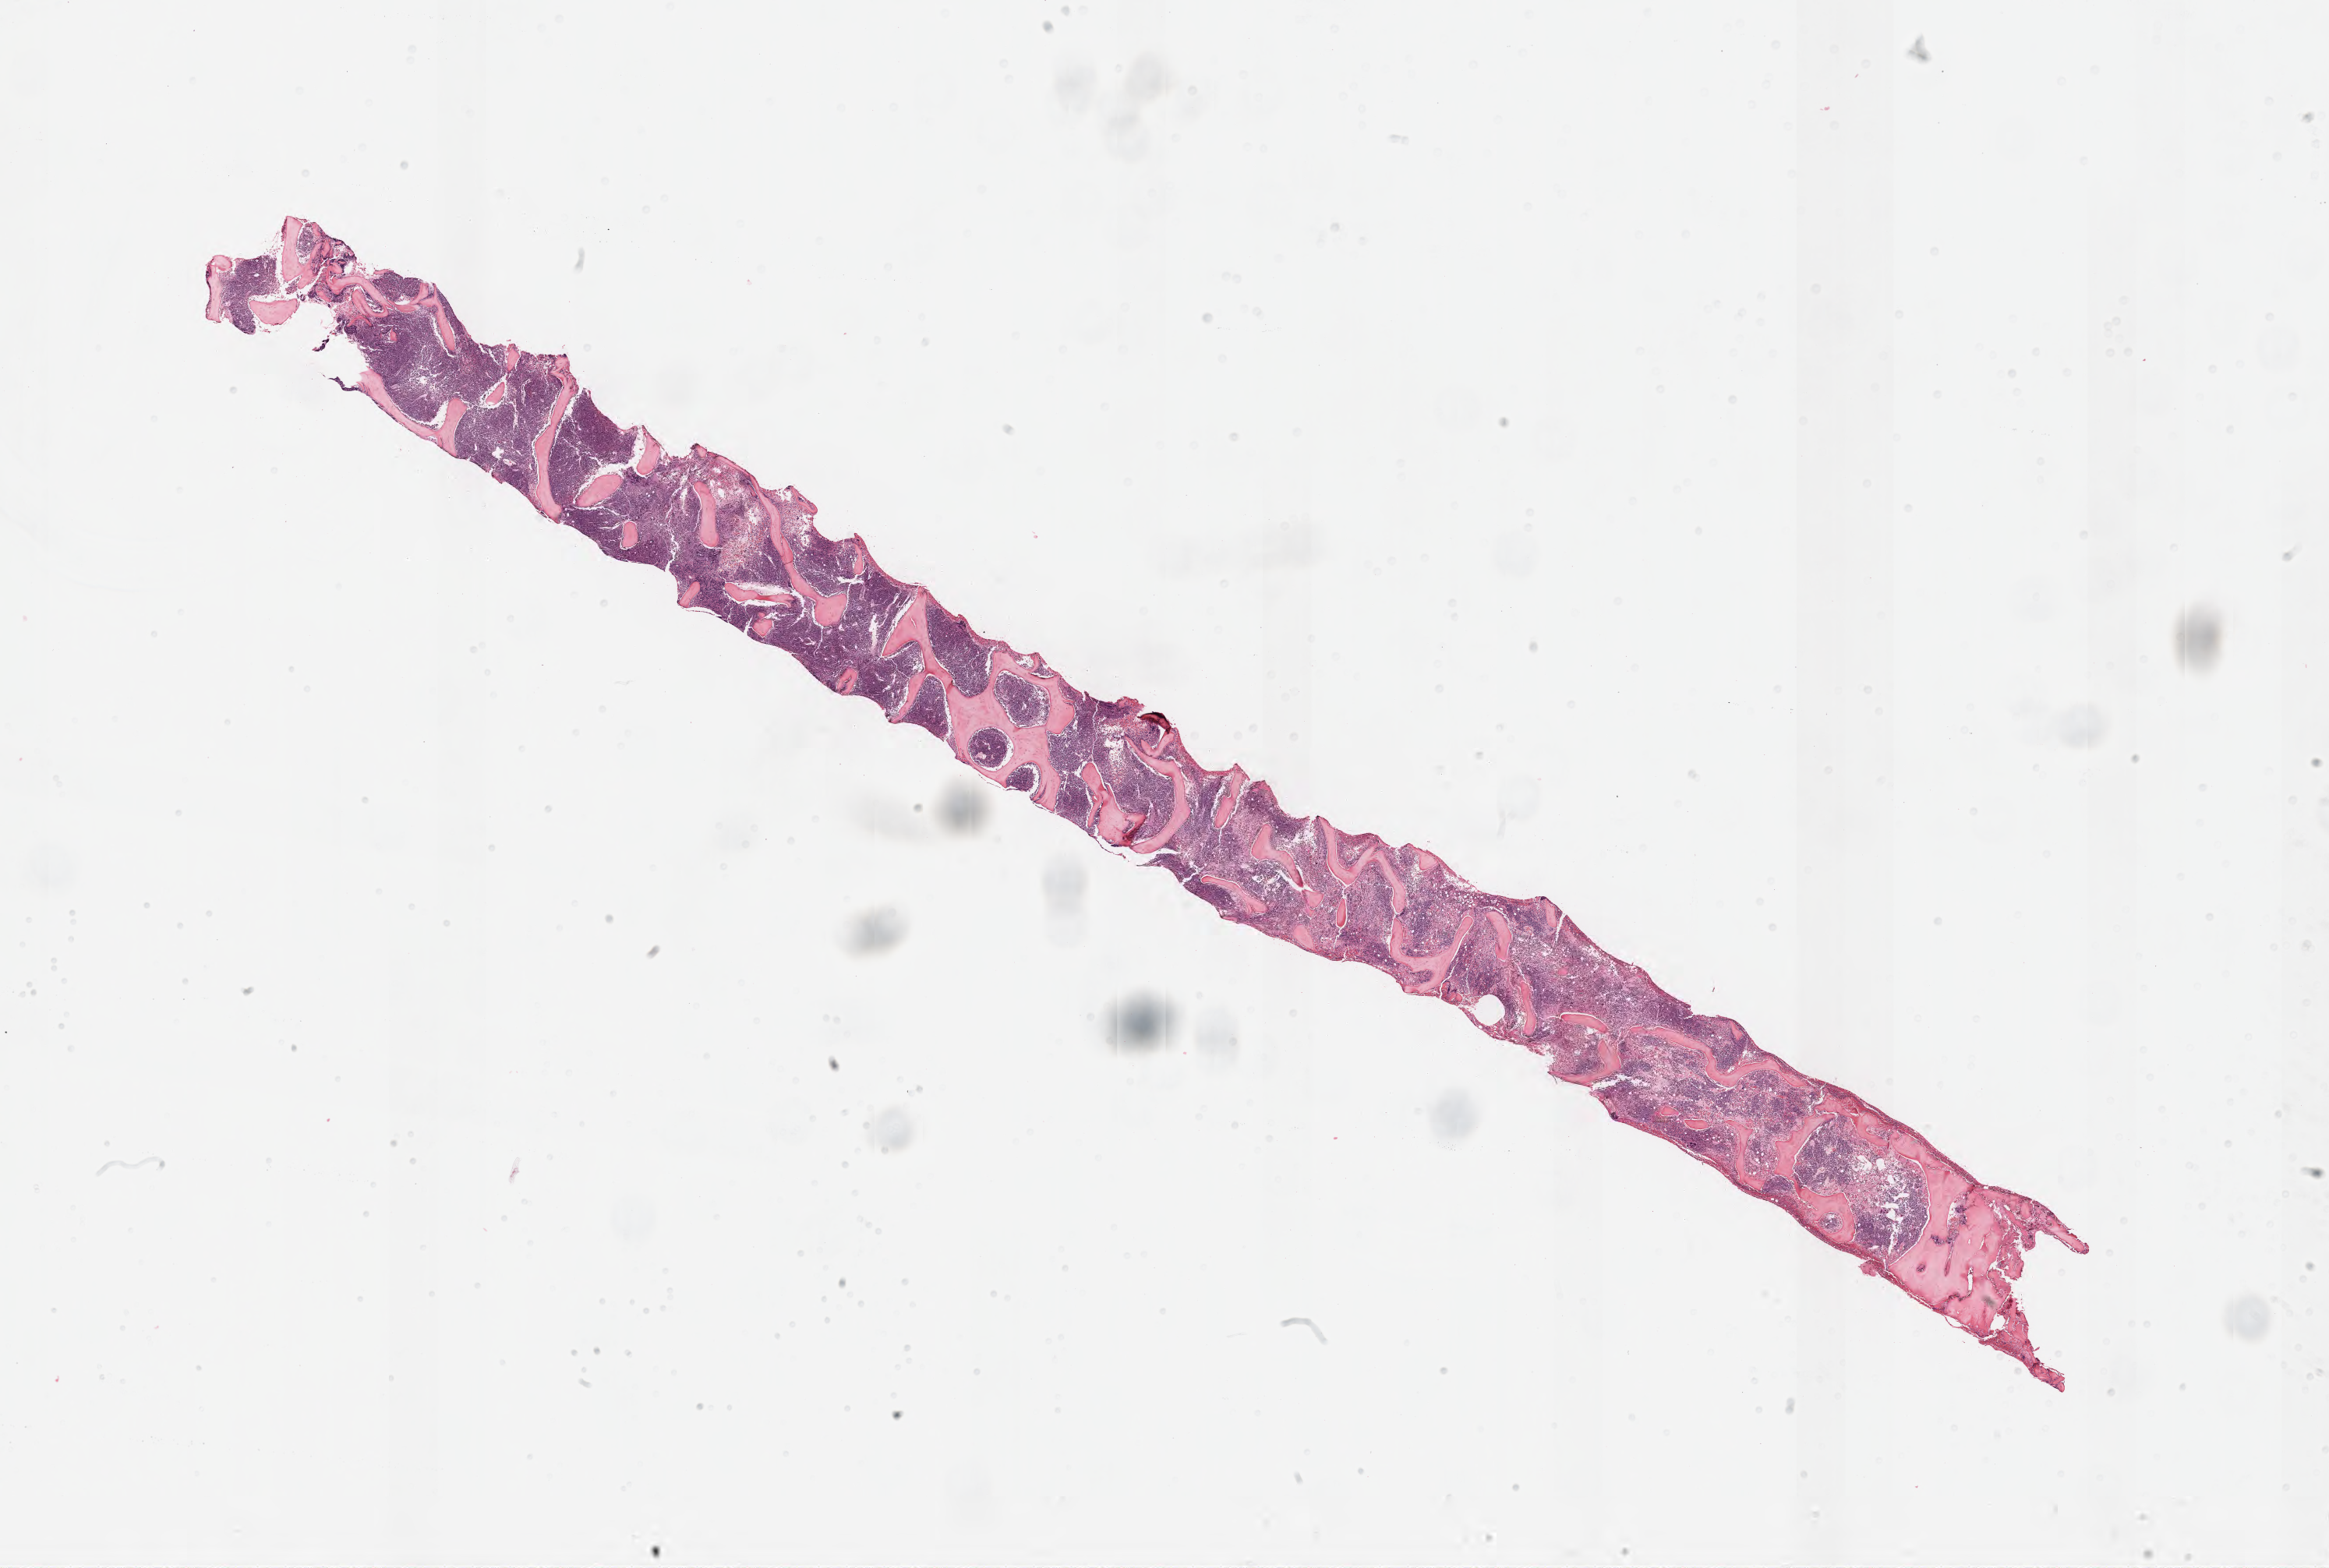
Whole-slide image, hematoxylin and eosin (H&E) stain — low-resolution overview of the scanned area, about 24.1 x 16.3 mm; specimen: tumor tissue; anatomic site: bone marrow. Patient: male, 18 years old.
Histologic diagnosis: Burkitt lymphoma, NOS.